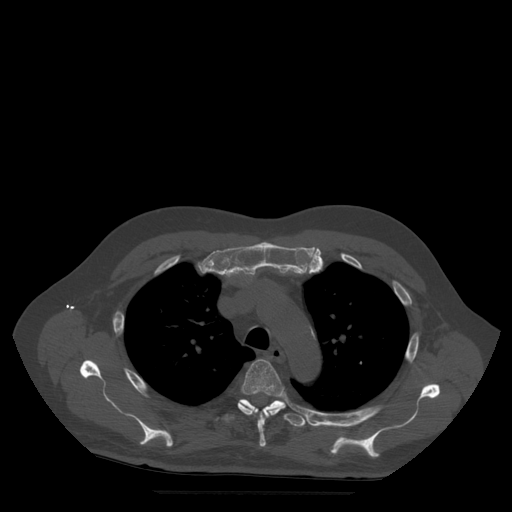
CT including the spine, one axial slice; position 385 of 522 along the scan axis; bone window (W 1800 / L 400 HU); 1.25 mm slice thickness; 512 × 512 image matrix. Patient age 72 years. From the clinical record (not read from this slice): primary cancer: prostate.
Outlined on this slice (semi-automatic segmentation, software-assisted and operator-edited):
- T4 vertebra: bounding box (x1, y1, x2, y2) in pixels: (238, 360, 287, 448)
- T5 vertebra: (233, 397, 312, 427)